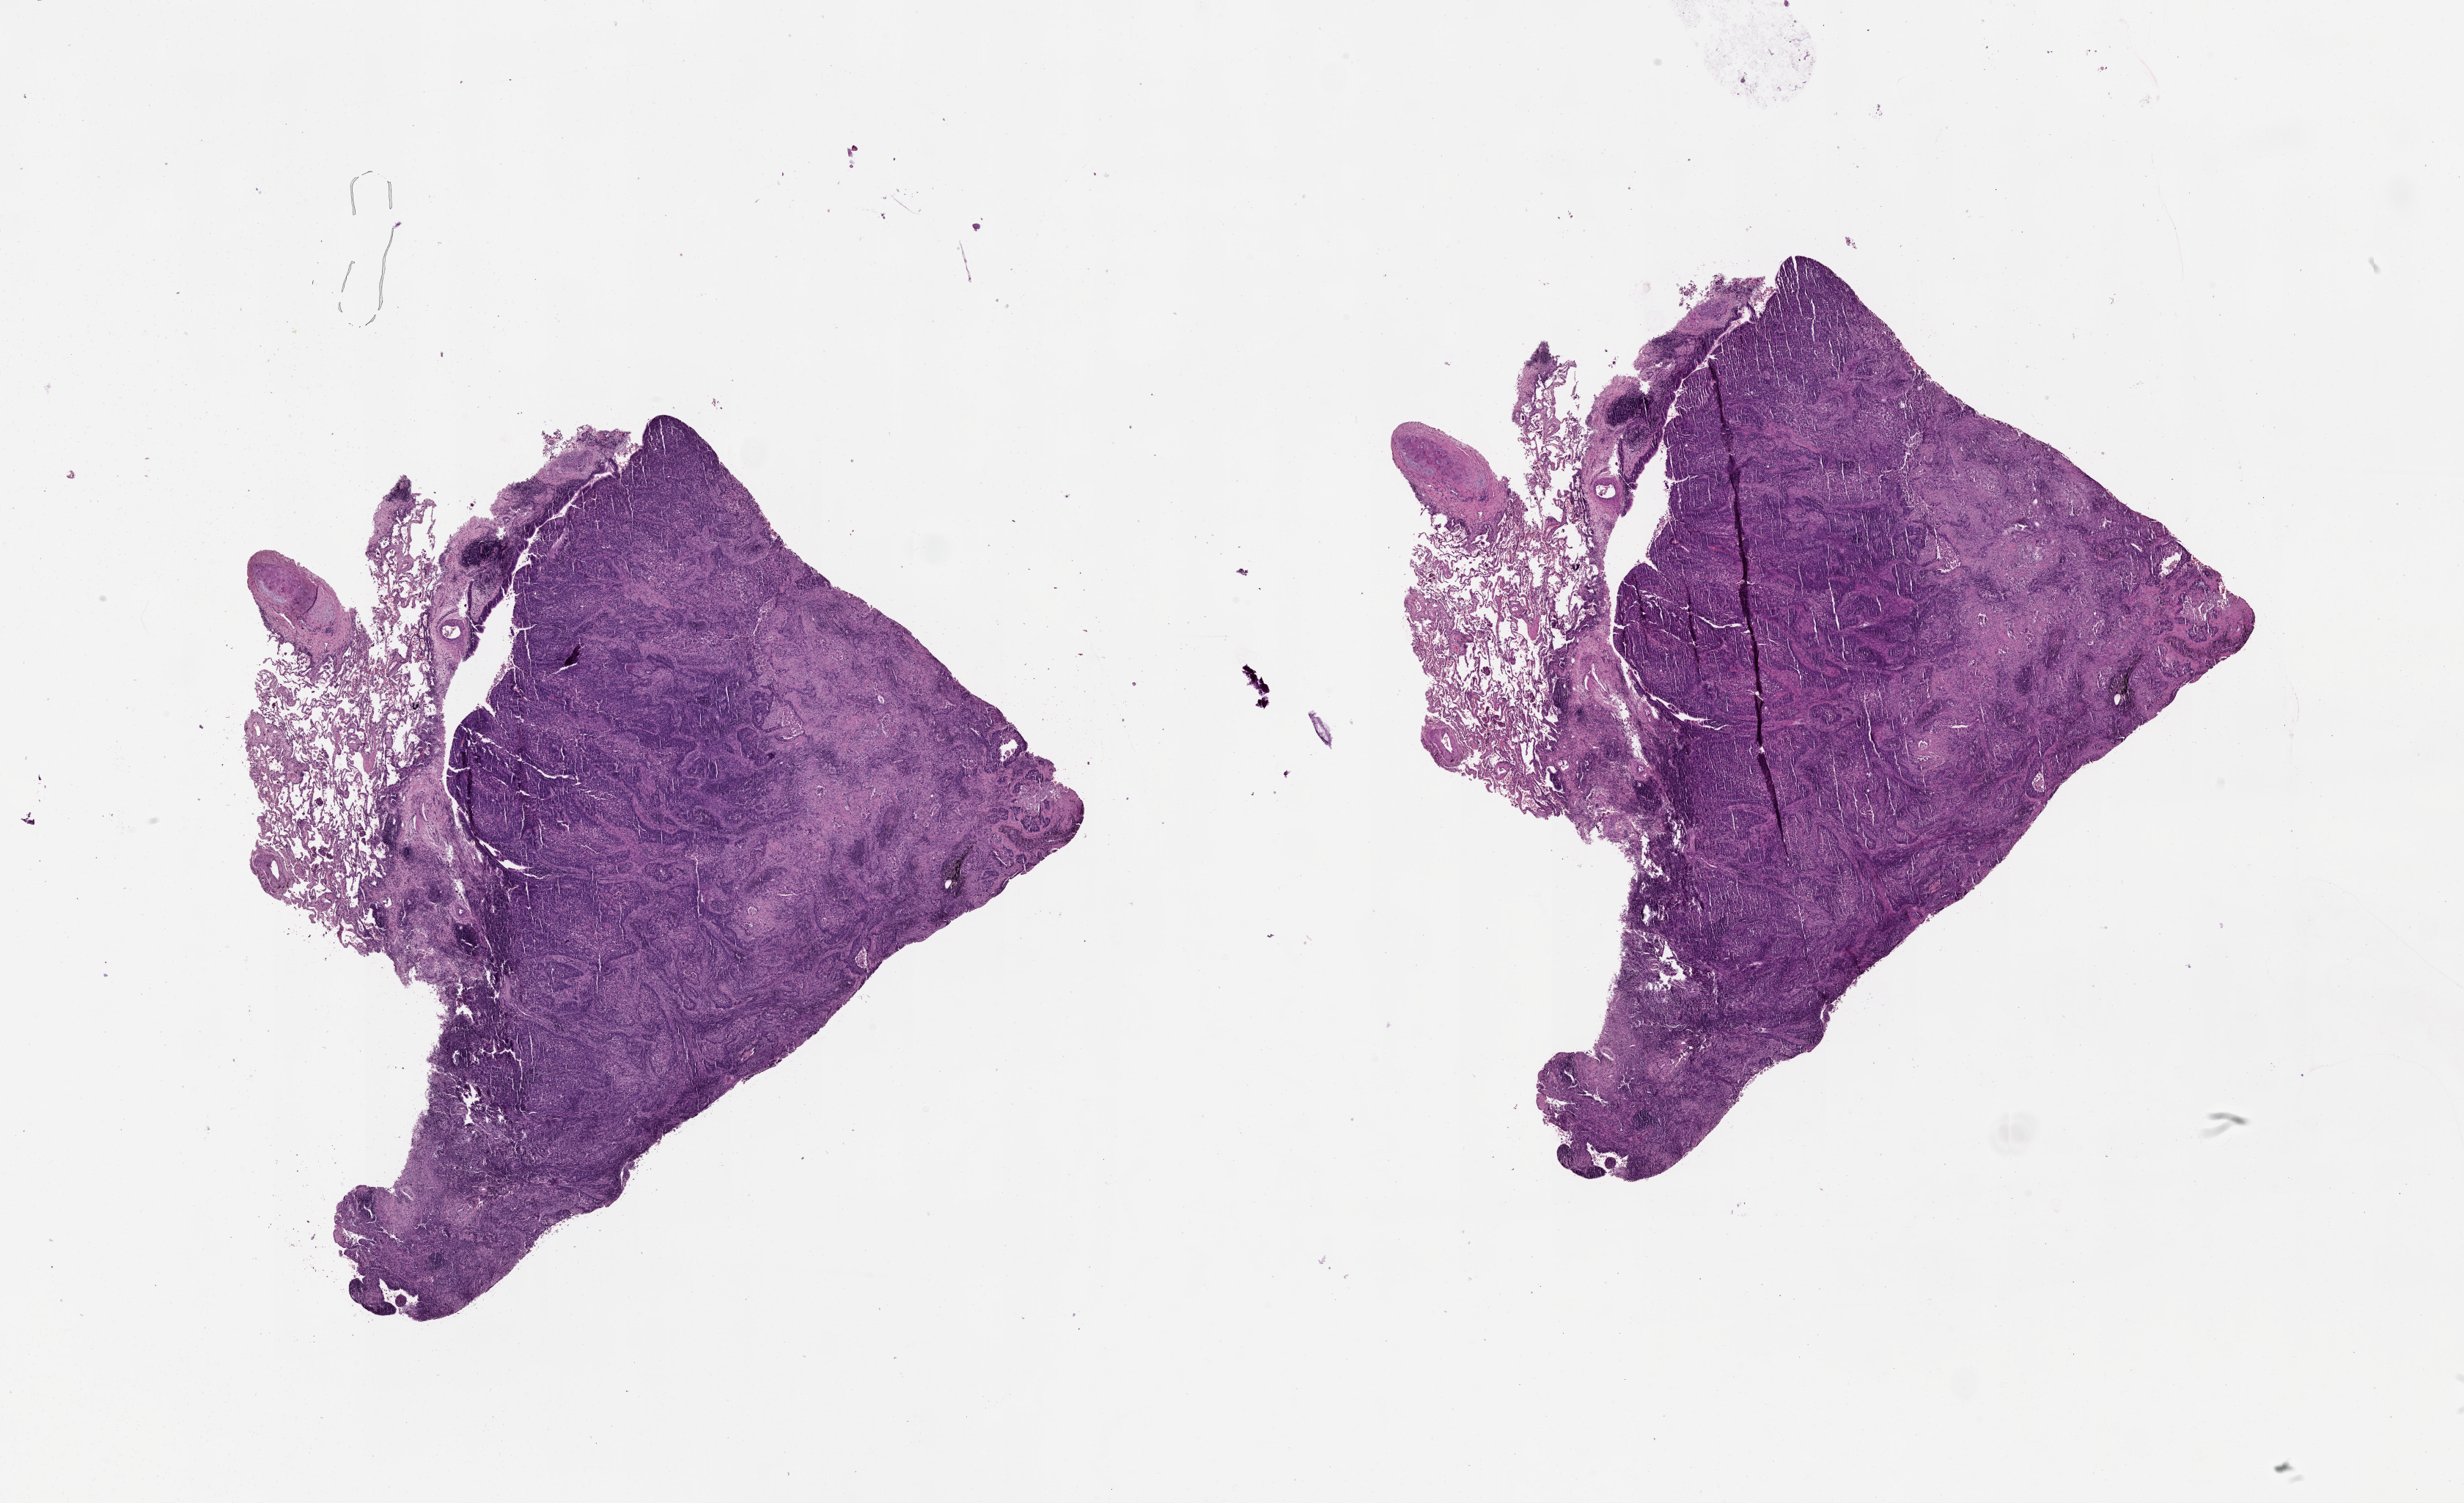
Whole-slide histology image, H&E-stained — shown as a low-resolution overview of the whole scanned area (about 27.1 x 16.5 mm, acquisition: 20x scan). Lung, tumour tissue. 66-year-old male patient.
Patient diagnosis (cohort enrolment): squamous cell carcinoma (lung).